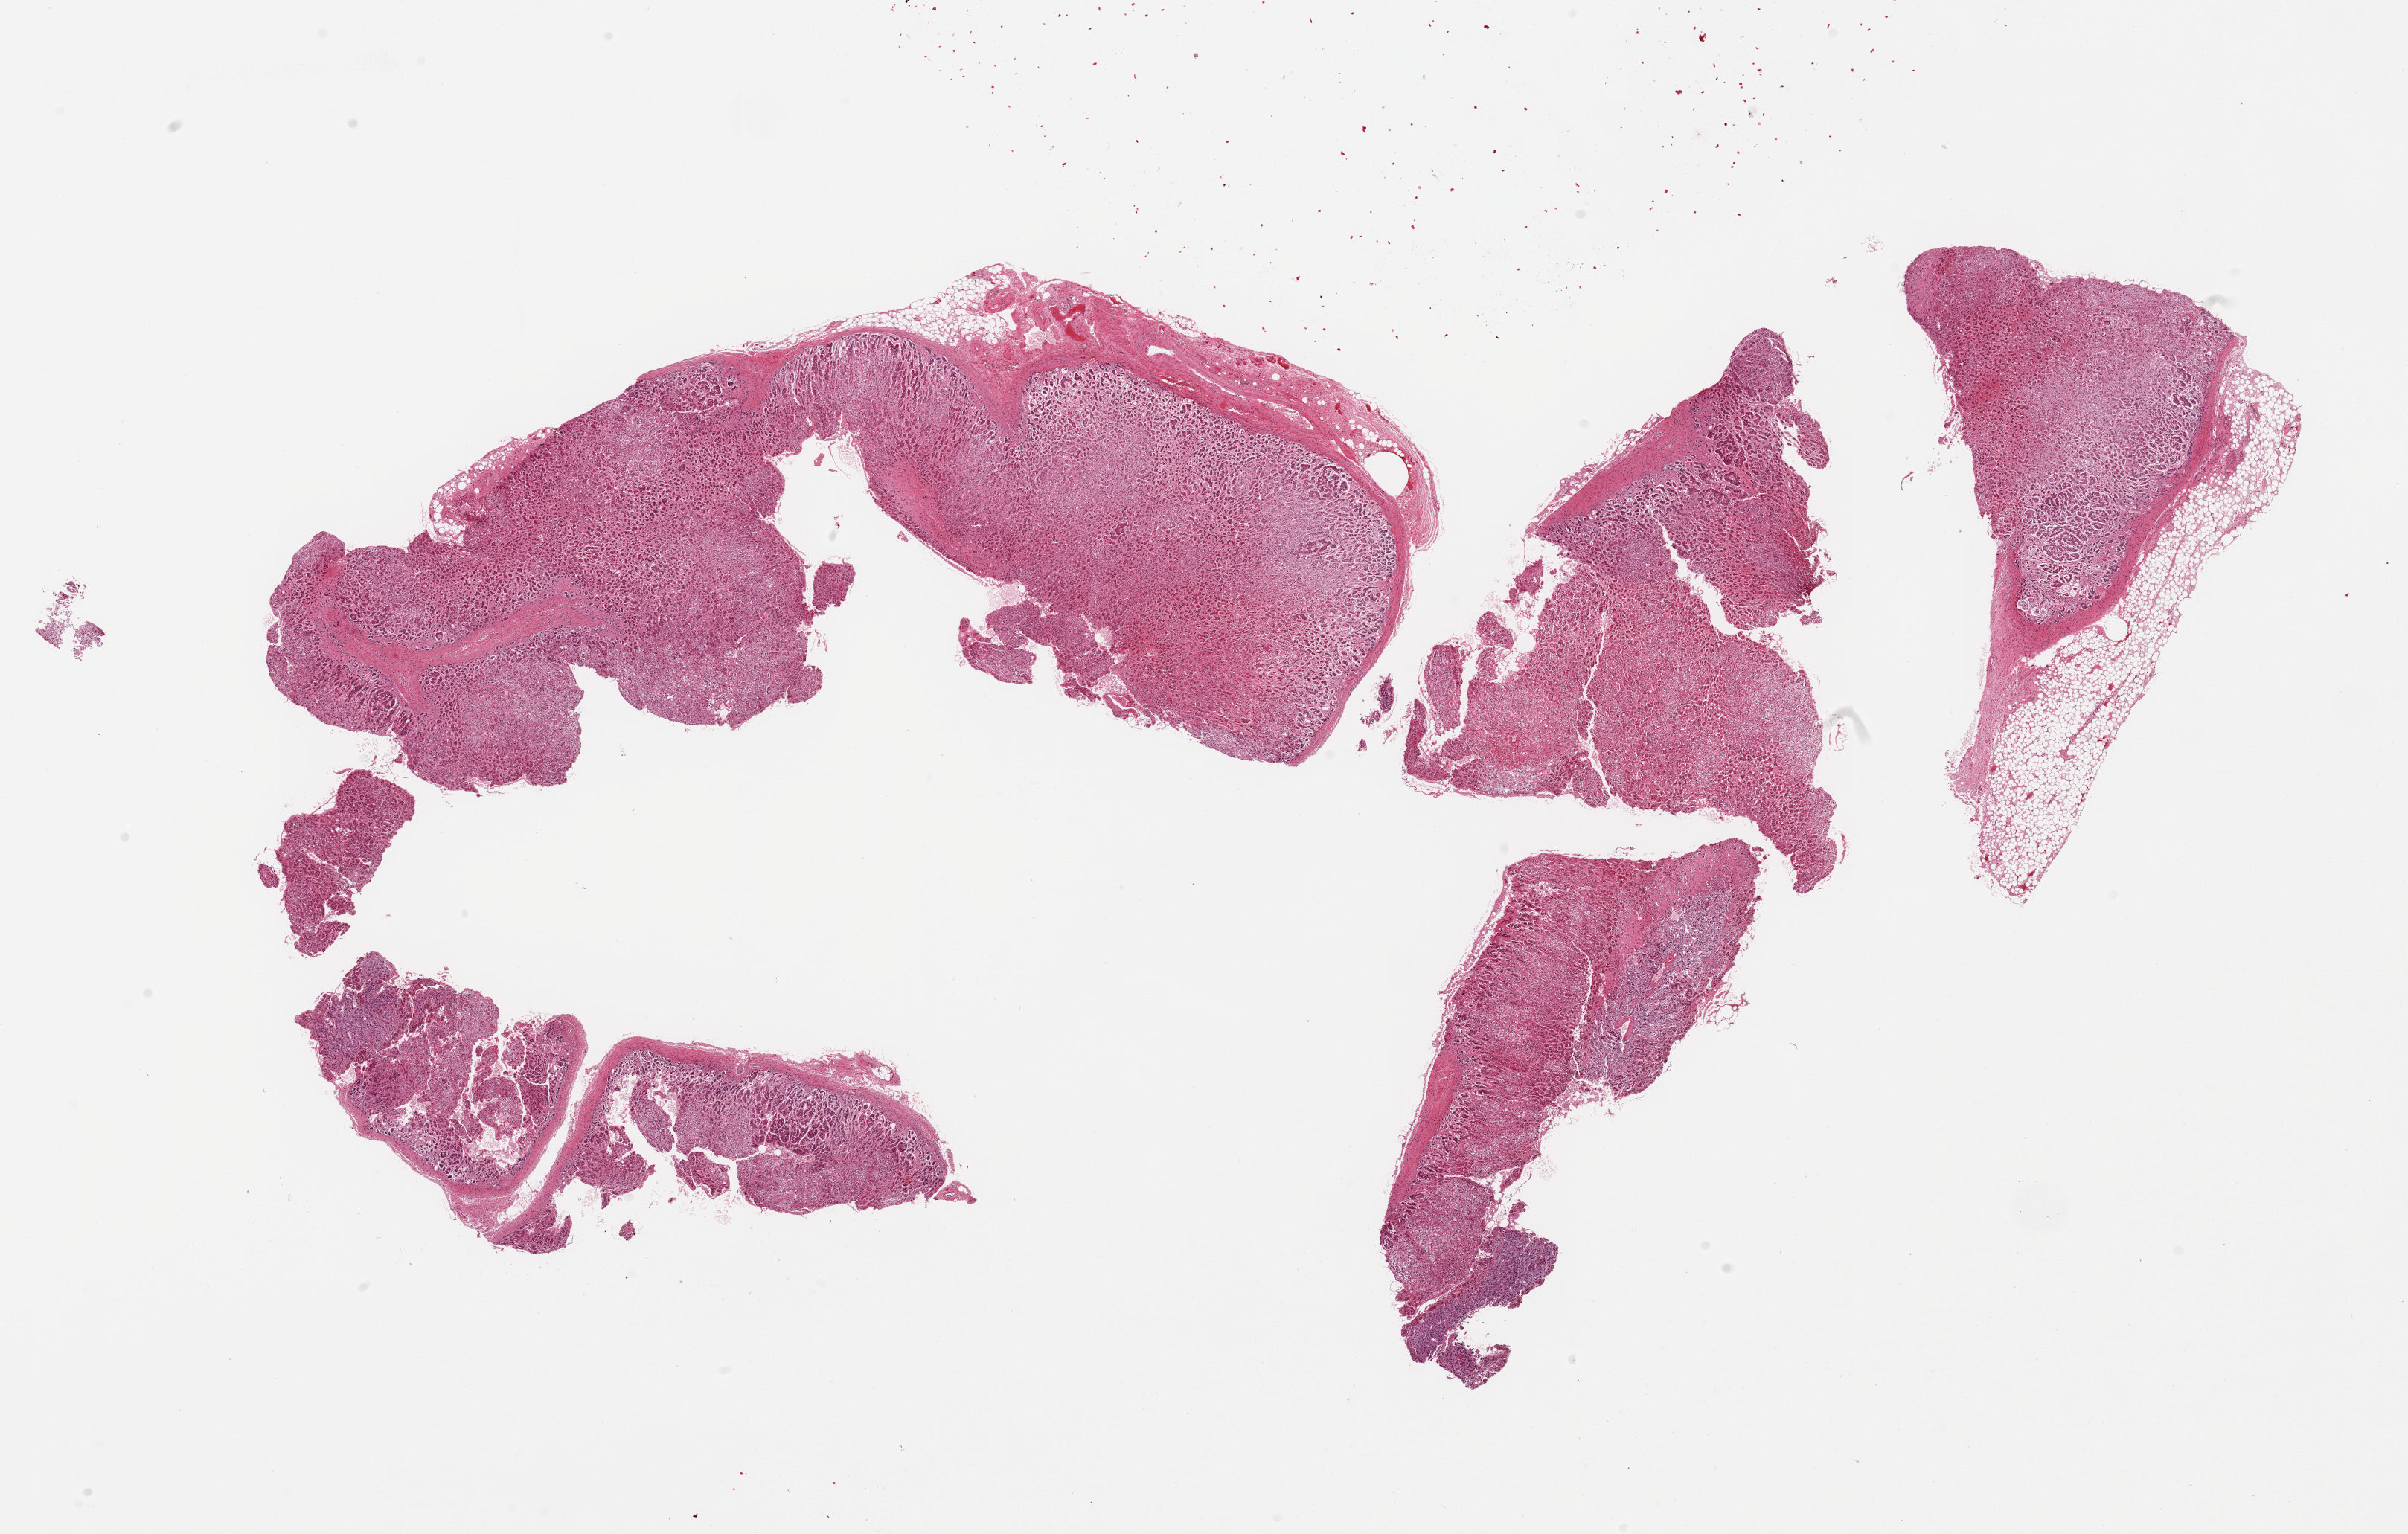
Hematoxylin and eosin (H&E) whole-slide image, brightfield — shown as a low-resolution overview of the whole scanned area (about 25.6 x 16.3 mm). PAXgene-fixed, paraffin-embedded tissue. Sampled site (target tissue): adrenal gland. Donor tissue sample.
Pathologist's review note for this sample: 2 pieces (fragmented); attached fat and vessels, up to 1x6mm; cortex and medulla.